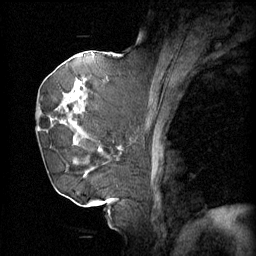
Breast MRI (dynamic contrast-enhanced), one sagittal slice. Slice 28 of 60 in the series (ordered by position). 4 images stored at this slice position (order not interpretable as contrast timing). 1.5 T. TE 4.2 ms, TR 11 ms. 2 mm slice thickness. 256 × 256 image matrix, field of view 220 × 220 mm. Patient: female, 72 years.
Outlined on this slice (semi-automatic segmentation, software-assisted and operator-edited):
- analysis volume of interest (the breast-tissue region the enhancement analysis was run in; not a lesion): bounding box [x1, y1, x2, y2] px = [43, 68, 109, 163]
- tumour enhancement mask (voxels above the 70 % enhancement threshold inside the analysis volume of interest): [43, 78, 109, 157]